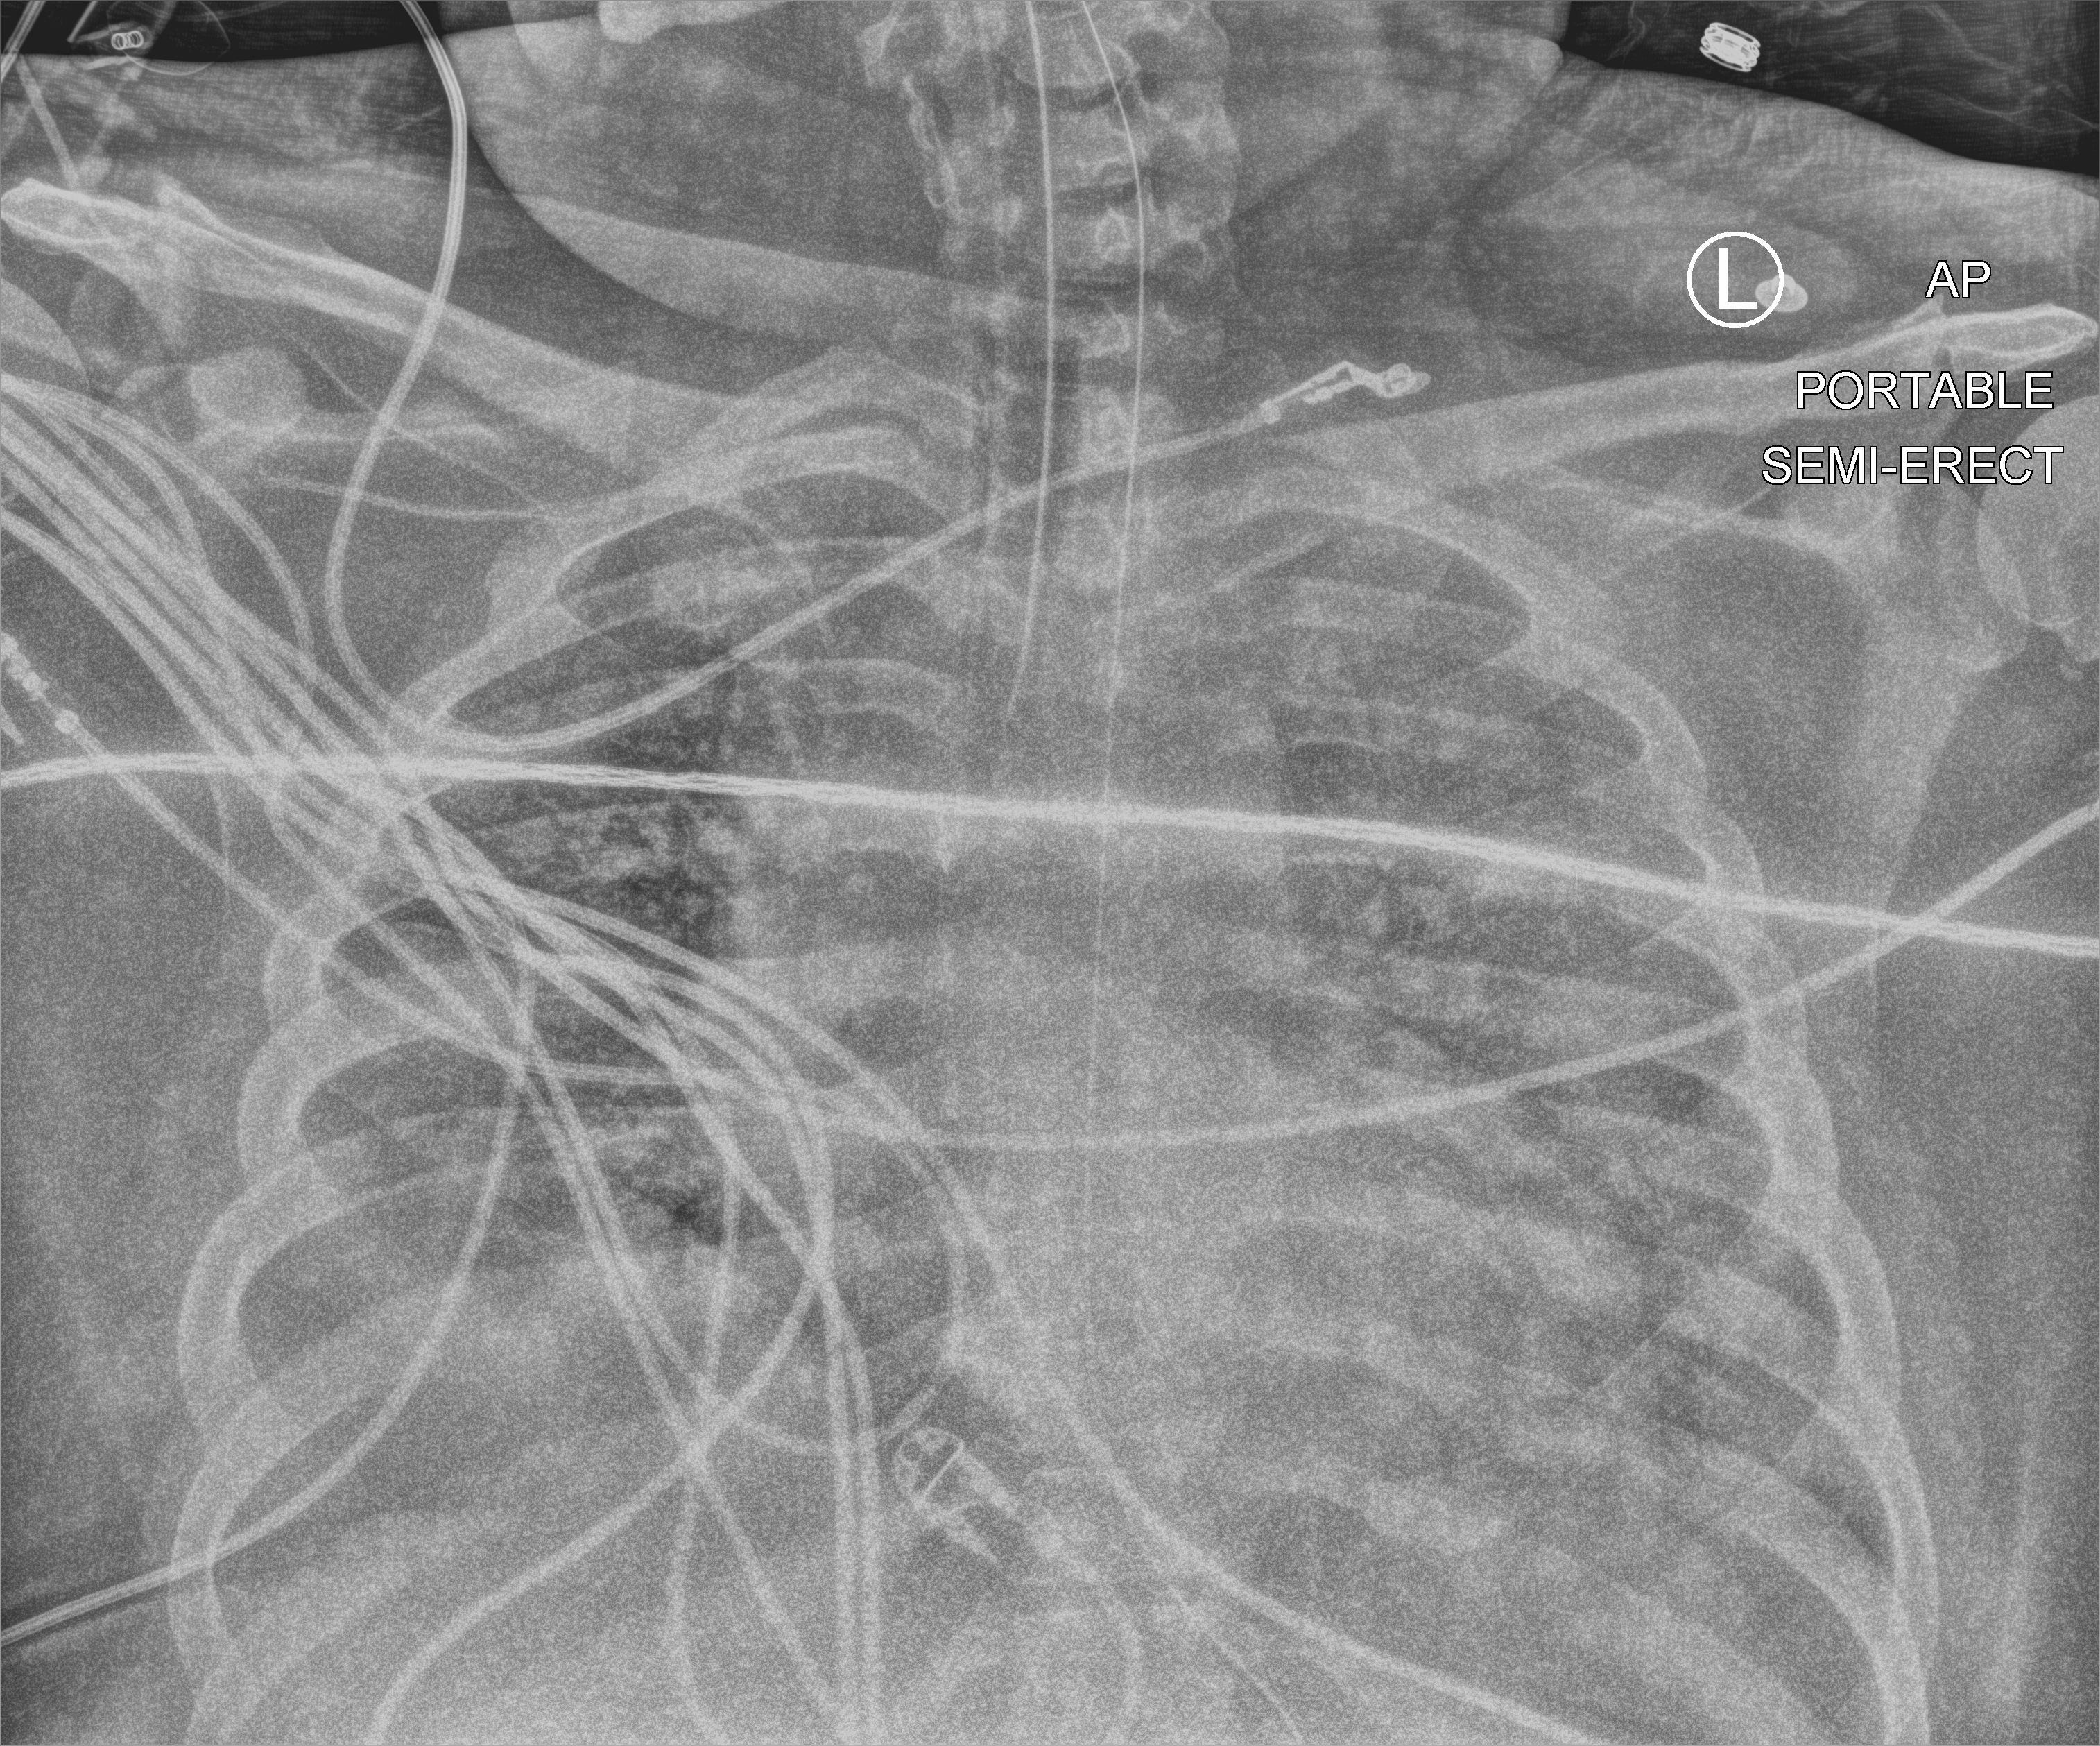
Portable chest radiograph, anteroposterior (AP) projection. Adult patient hospitalised with COVID-19, age 18–59 years.
From the hospital-stay record, not from the radiograph (when in the stay this image was taken is not recorded):
- admitted to intensive care during this hospital stay: yes
- length of hospital stay: 10 days
- mechanically ventilated during this hospital stay: yes